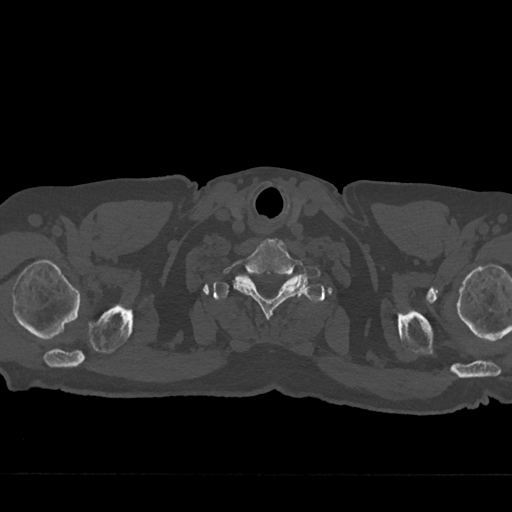
CT including the spine, one axial slice. Position 683 of 797 along the scan axis. Bone window (W 1800 / L 400 HU). 512 × 512 image matrix, field of view 377 × 377 mm. Patient: male, 75 years. From the clinical record (not read from this slice): primary cancer: renal; vertebrae with lytic lesions (as recorded): T4.
Structures marked on this image (semi-automatically segmented with operator editing):
- T1 vertebra: bounding box [x1, y1, x2, y2] px = [213, 275, 304, 300]